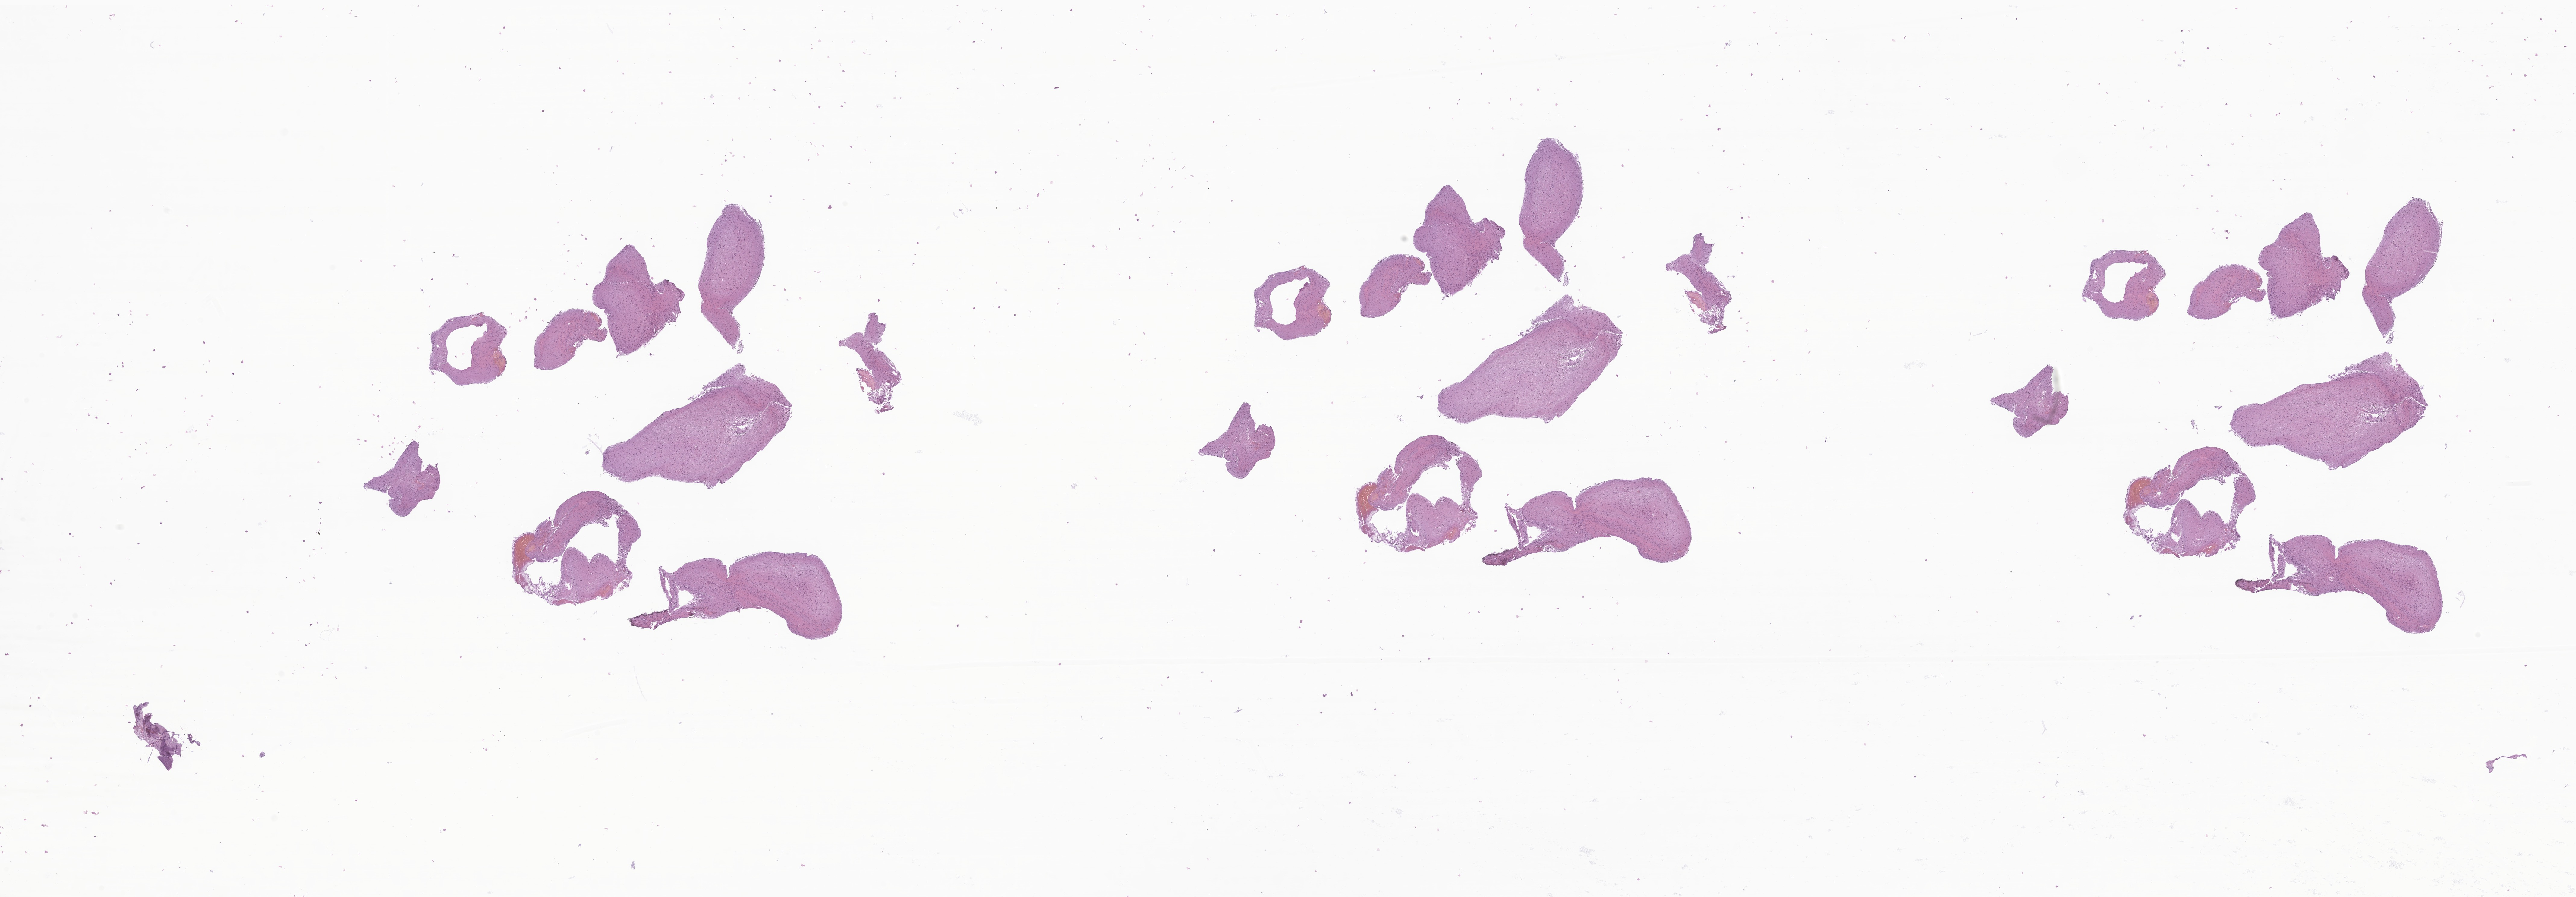
Whole-slide image, haematoxylin and eosin stain of tumor tissue from the cerebral ventricle — low-resolution overview of the scanned area, about 36.0 x 12.5 mm. FFPE section. Female patient, age 172 months.
Recorded diagnosis: Neoplasm, malignant.